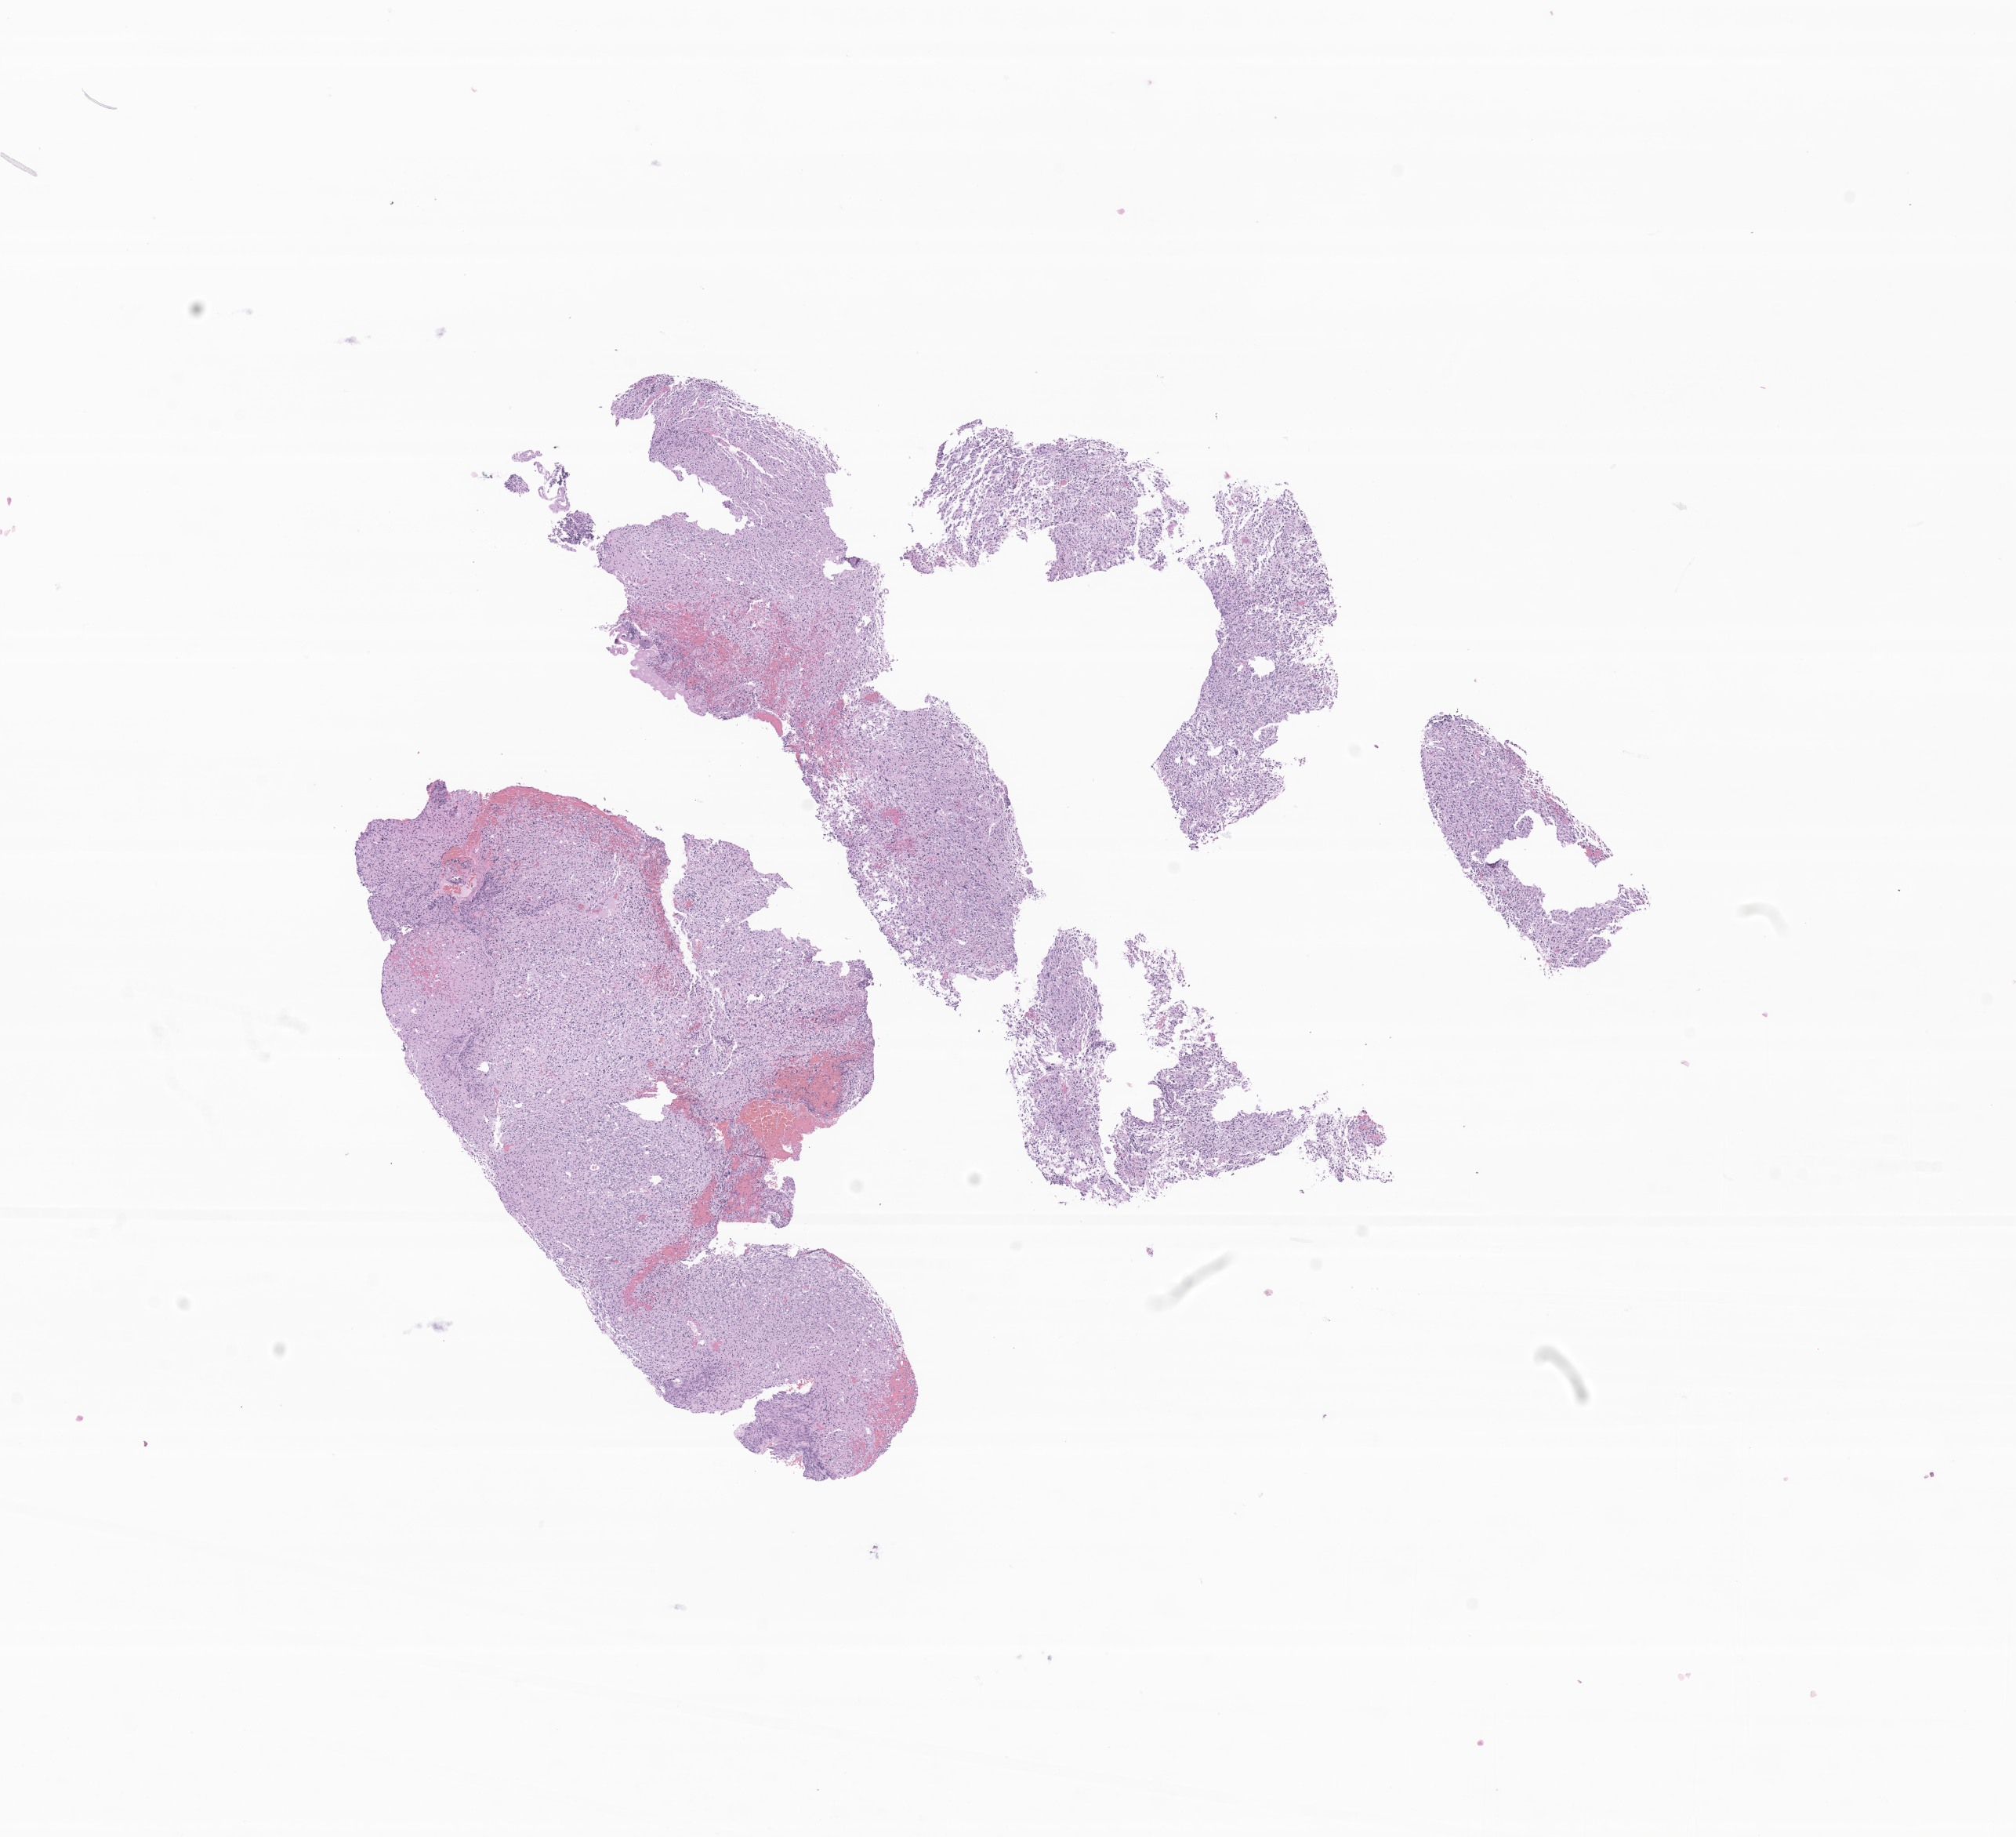
H&E whole-slide image of tumor tissue from the cerebrum — shown as a low-resolution overview of the whole scanned area (about 10.8 x 9.9 mm); FFPE section. Patient male; age 183 months (15 years 3 months).
- diagnosis (ICD-O-3 morphology term): Glioma, malignant